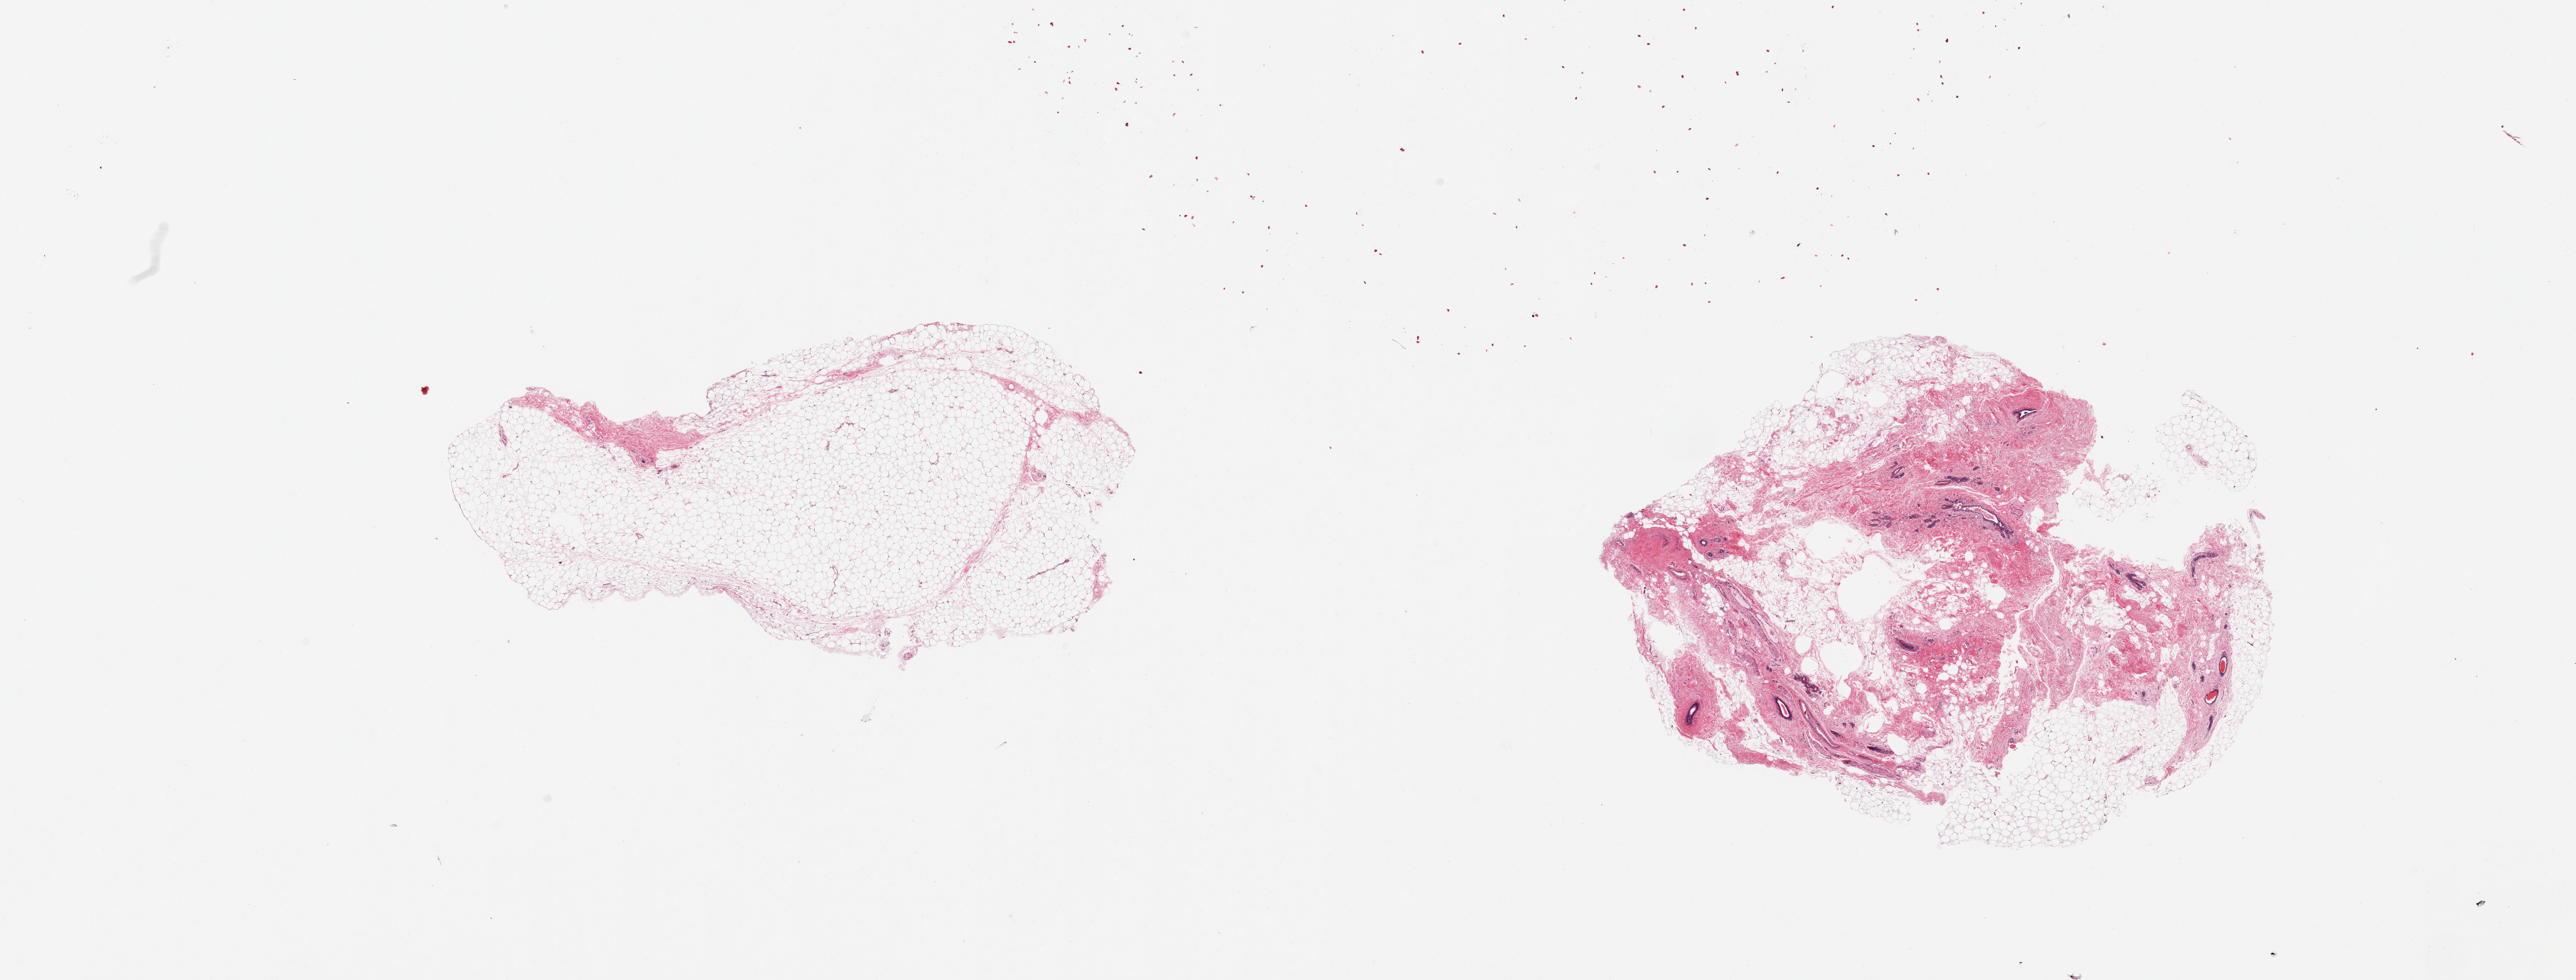
Hematoxylin and eosin (H&E) whole-slide image, low-resolution overview of the scanned area, about 28.5 x 10.9 mm. PAXgene-fixed paraffin-embedded (PFPE) section. Sampled site (target tissue): breast. Donor tissue sample. Donor sex: female.
- review note (as recorded): 2 pieces, mainly fibroadipose tissue, a few ductal elements present